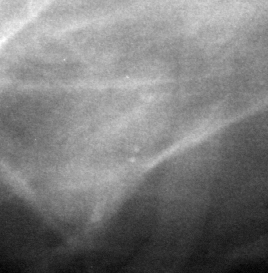
Region of interest cut from a scanned film mammogram (one marked finding), right breast, MLO view.
Finding: mass, shape oval, margins circumscribed / ill defined; BI-RADS assessment category 4; subtlety rating 2 on a 1 (subtle) to 5 (obvious) scale; pathology (as recorded): benign.